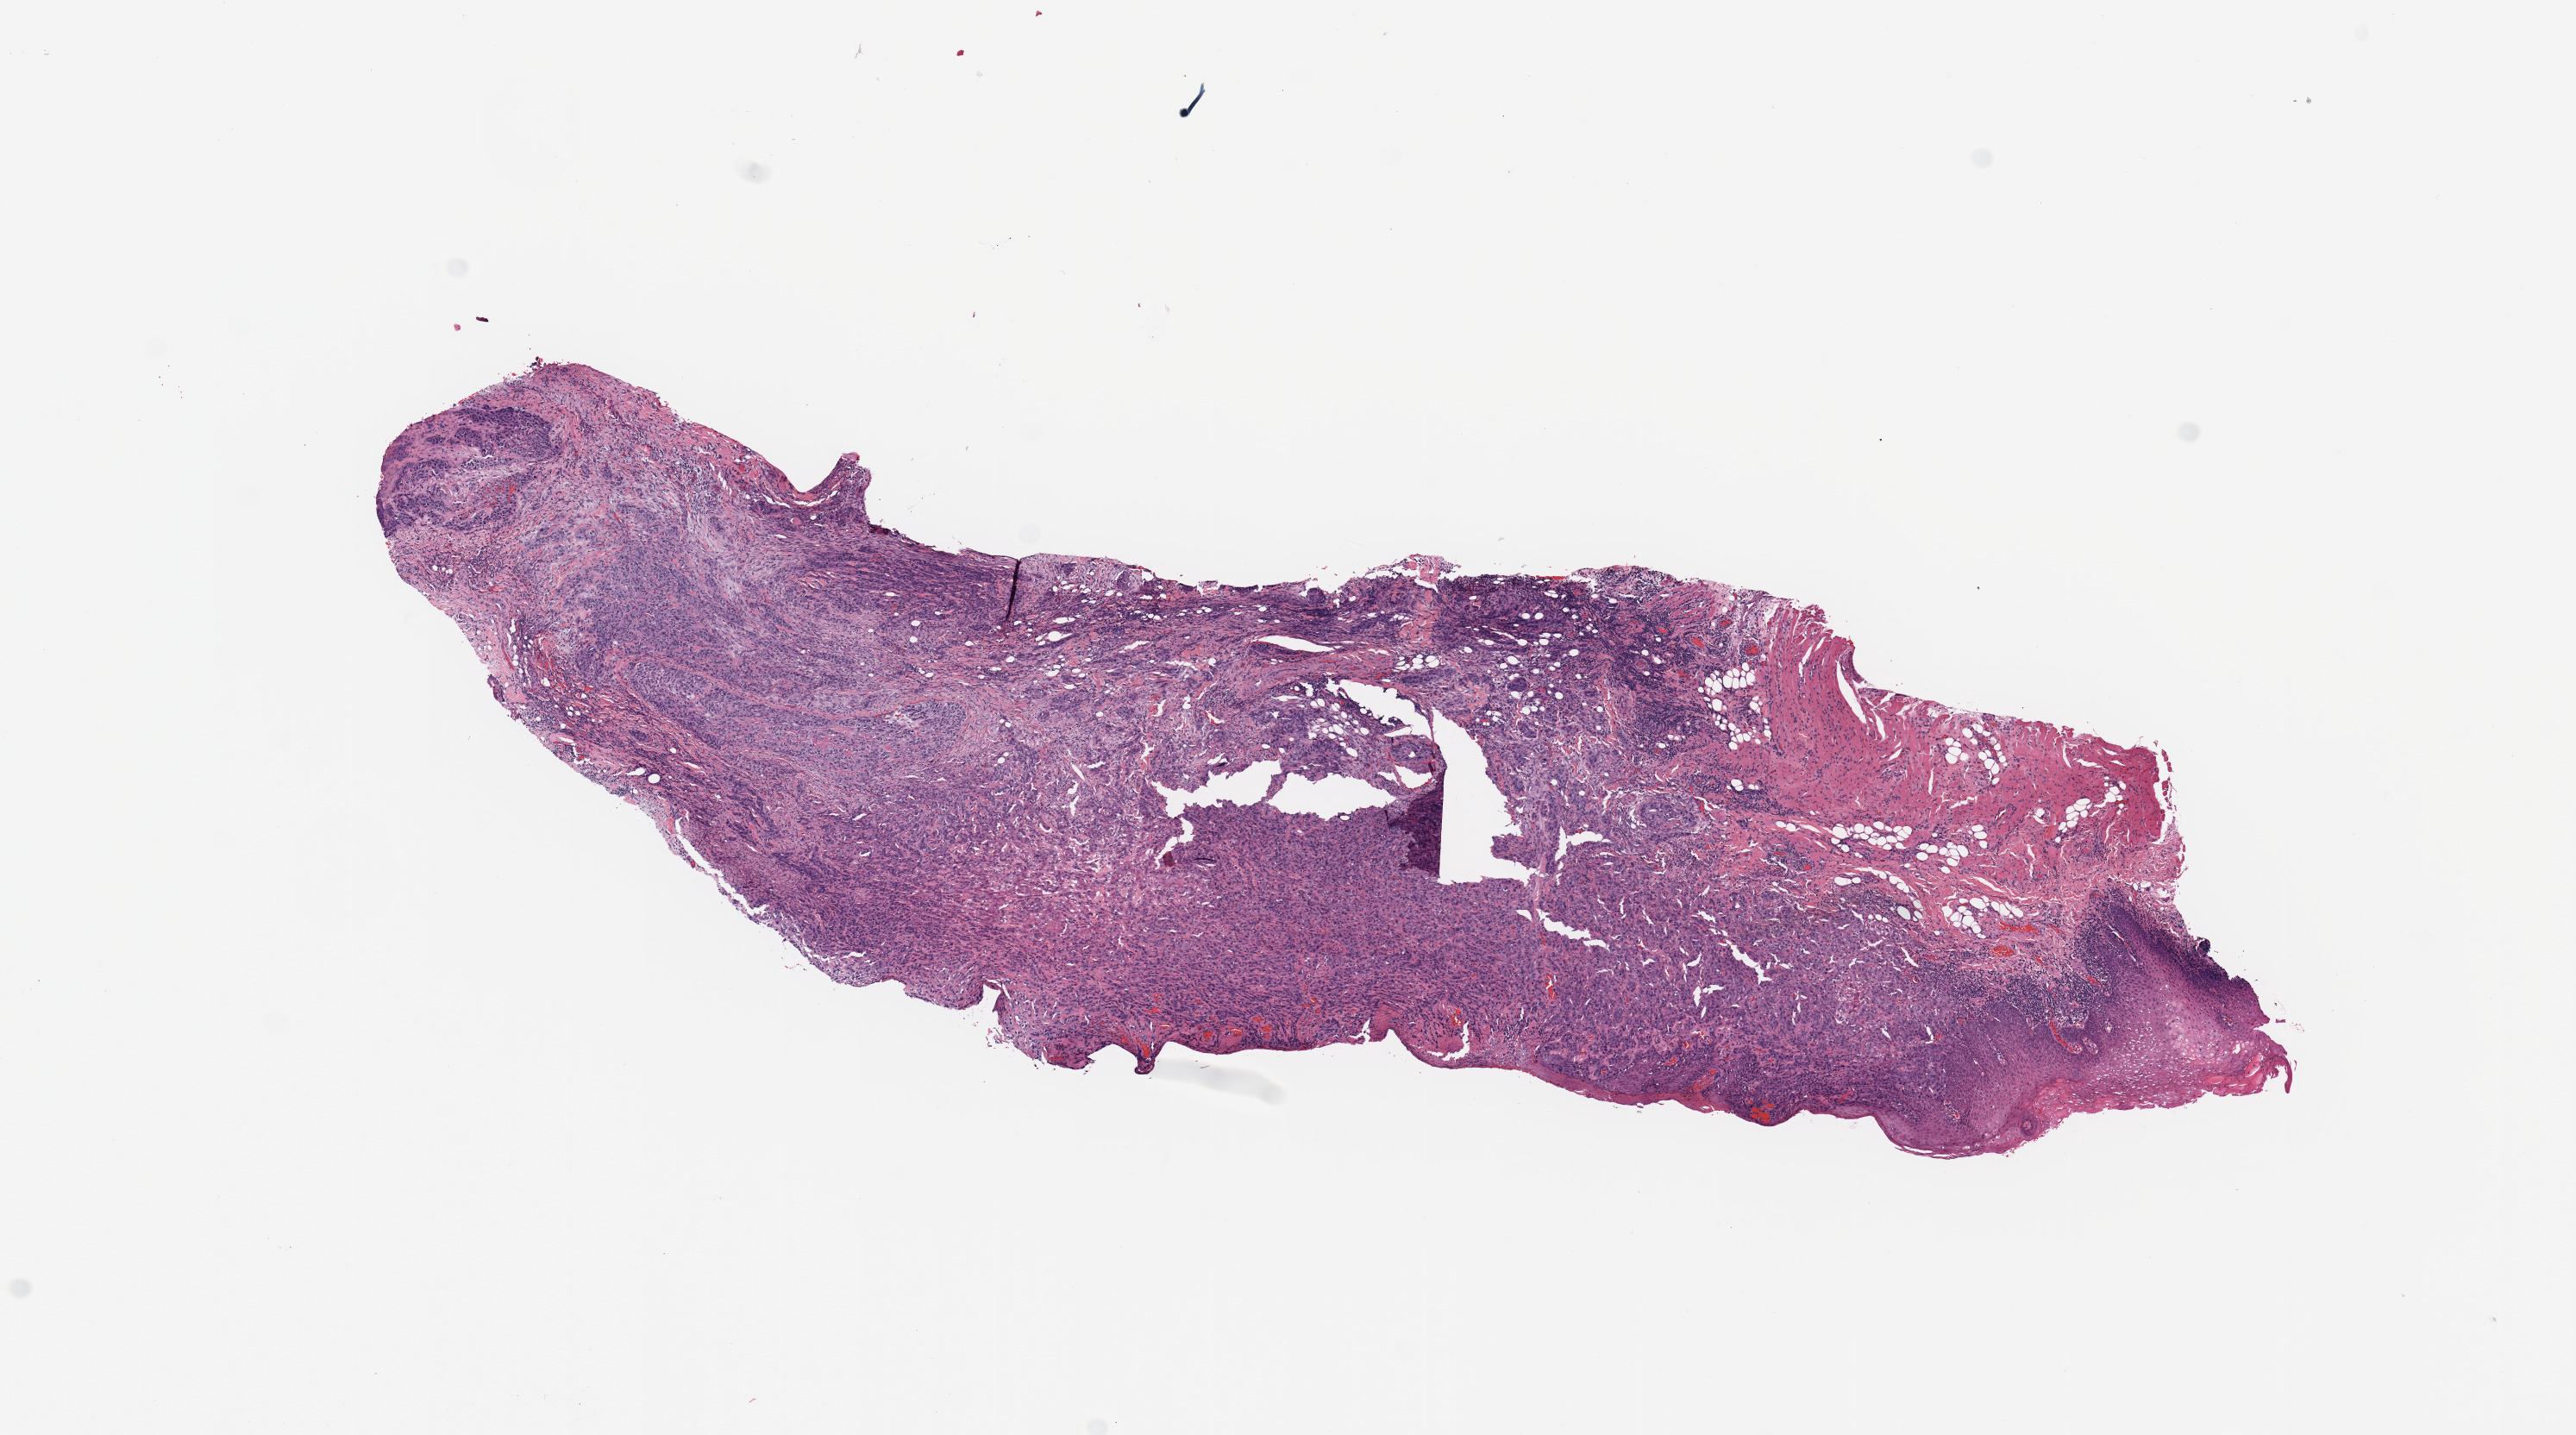
Digitized Hematoxylin and eosin (H&E) stained tissue section (whole slide), a low-resolution overview of the entire scanned area, about 11.8 x 6.6 mm. Head and neck, tissue type not recorded. Male, 56 y/o.
Patient diagnosis: Squamous cell carcinoma, NOS (floor of mouth, NOS).